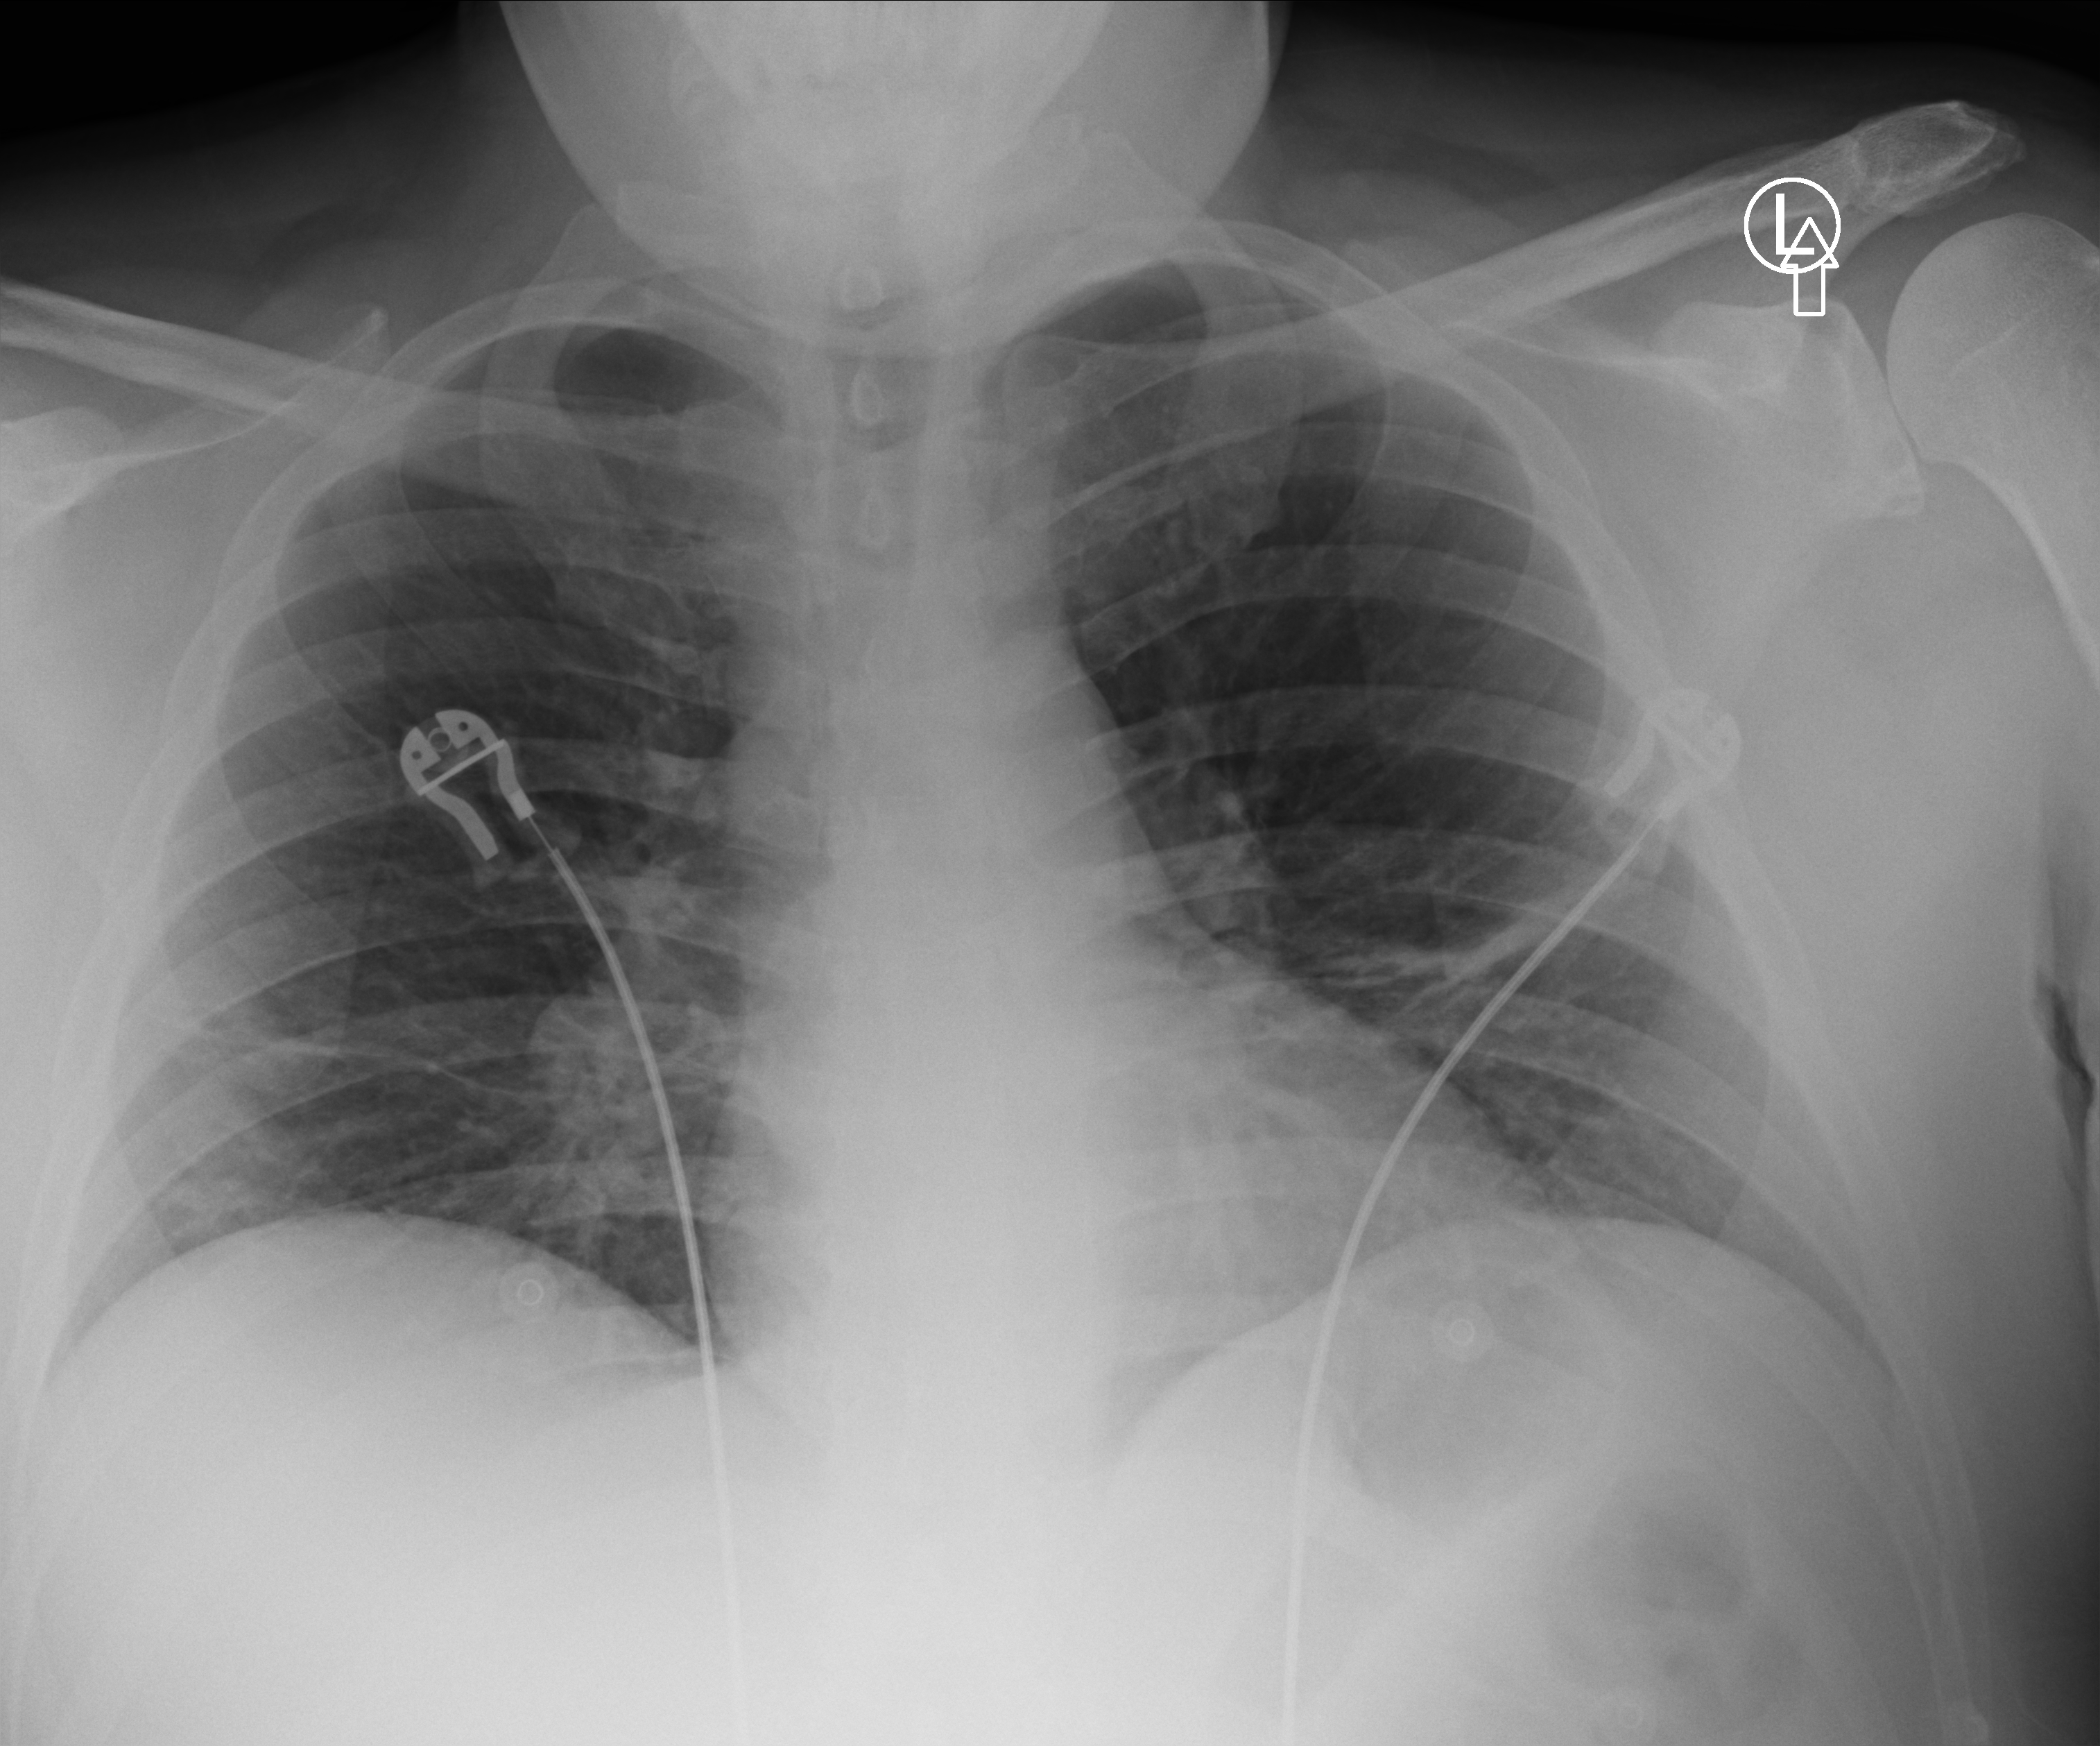
Bedside chest radiograph (computed radiography); anteroposterior (AP) projection. Patient hospitalised with COVID-19; male, aged 18–59 years.
From the hospital-stay record, not from the radiograph (when in the stay this image was taken is not recorded): admitted to intensive care during this hospital stay: no; other chronic lung disease (admission record): no.